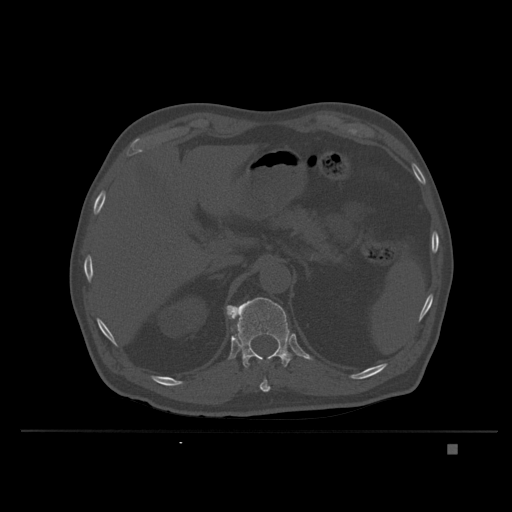
CT including the spine, one axial slice; position 163 of 435 along the scan axis; bone window (W 1800 / L 400 HU); 1.5 mm slice thickness; 512 × 512 image matrix, field of view 434 × 434 mm. Male patient, age 73 years. Case-level facts recorded for this patient, not image findings: primary cancer: skin.
Outlined on this slice (semi-automatically segmented with operator editing):
- T11 vertebra: bounding box (x1, y1, x2, y2) in pixels: (258, 361, 271, 392)
- T12 vertebra: (226, 297, 292, 368)